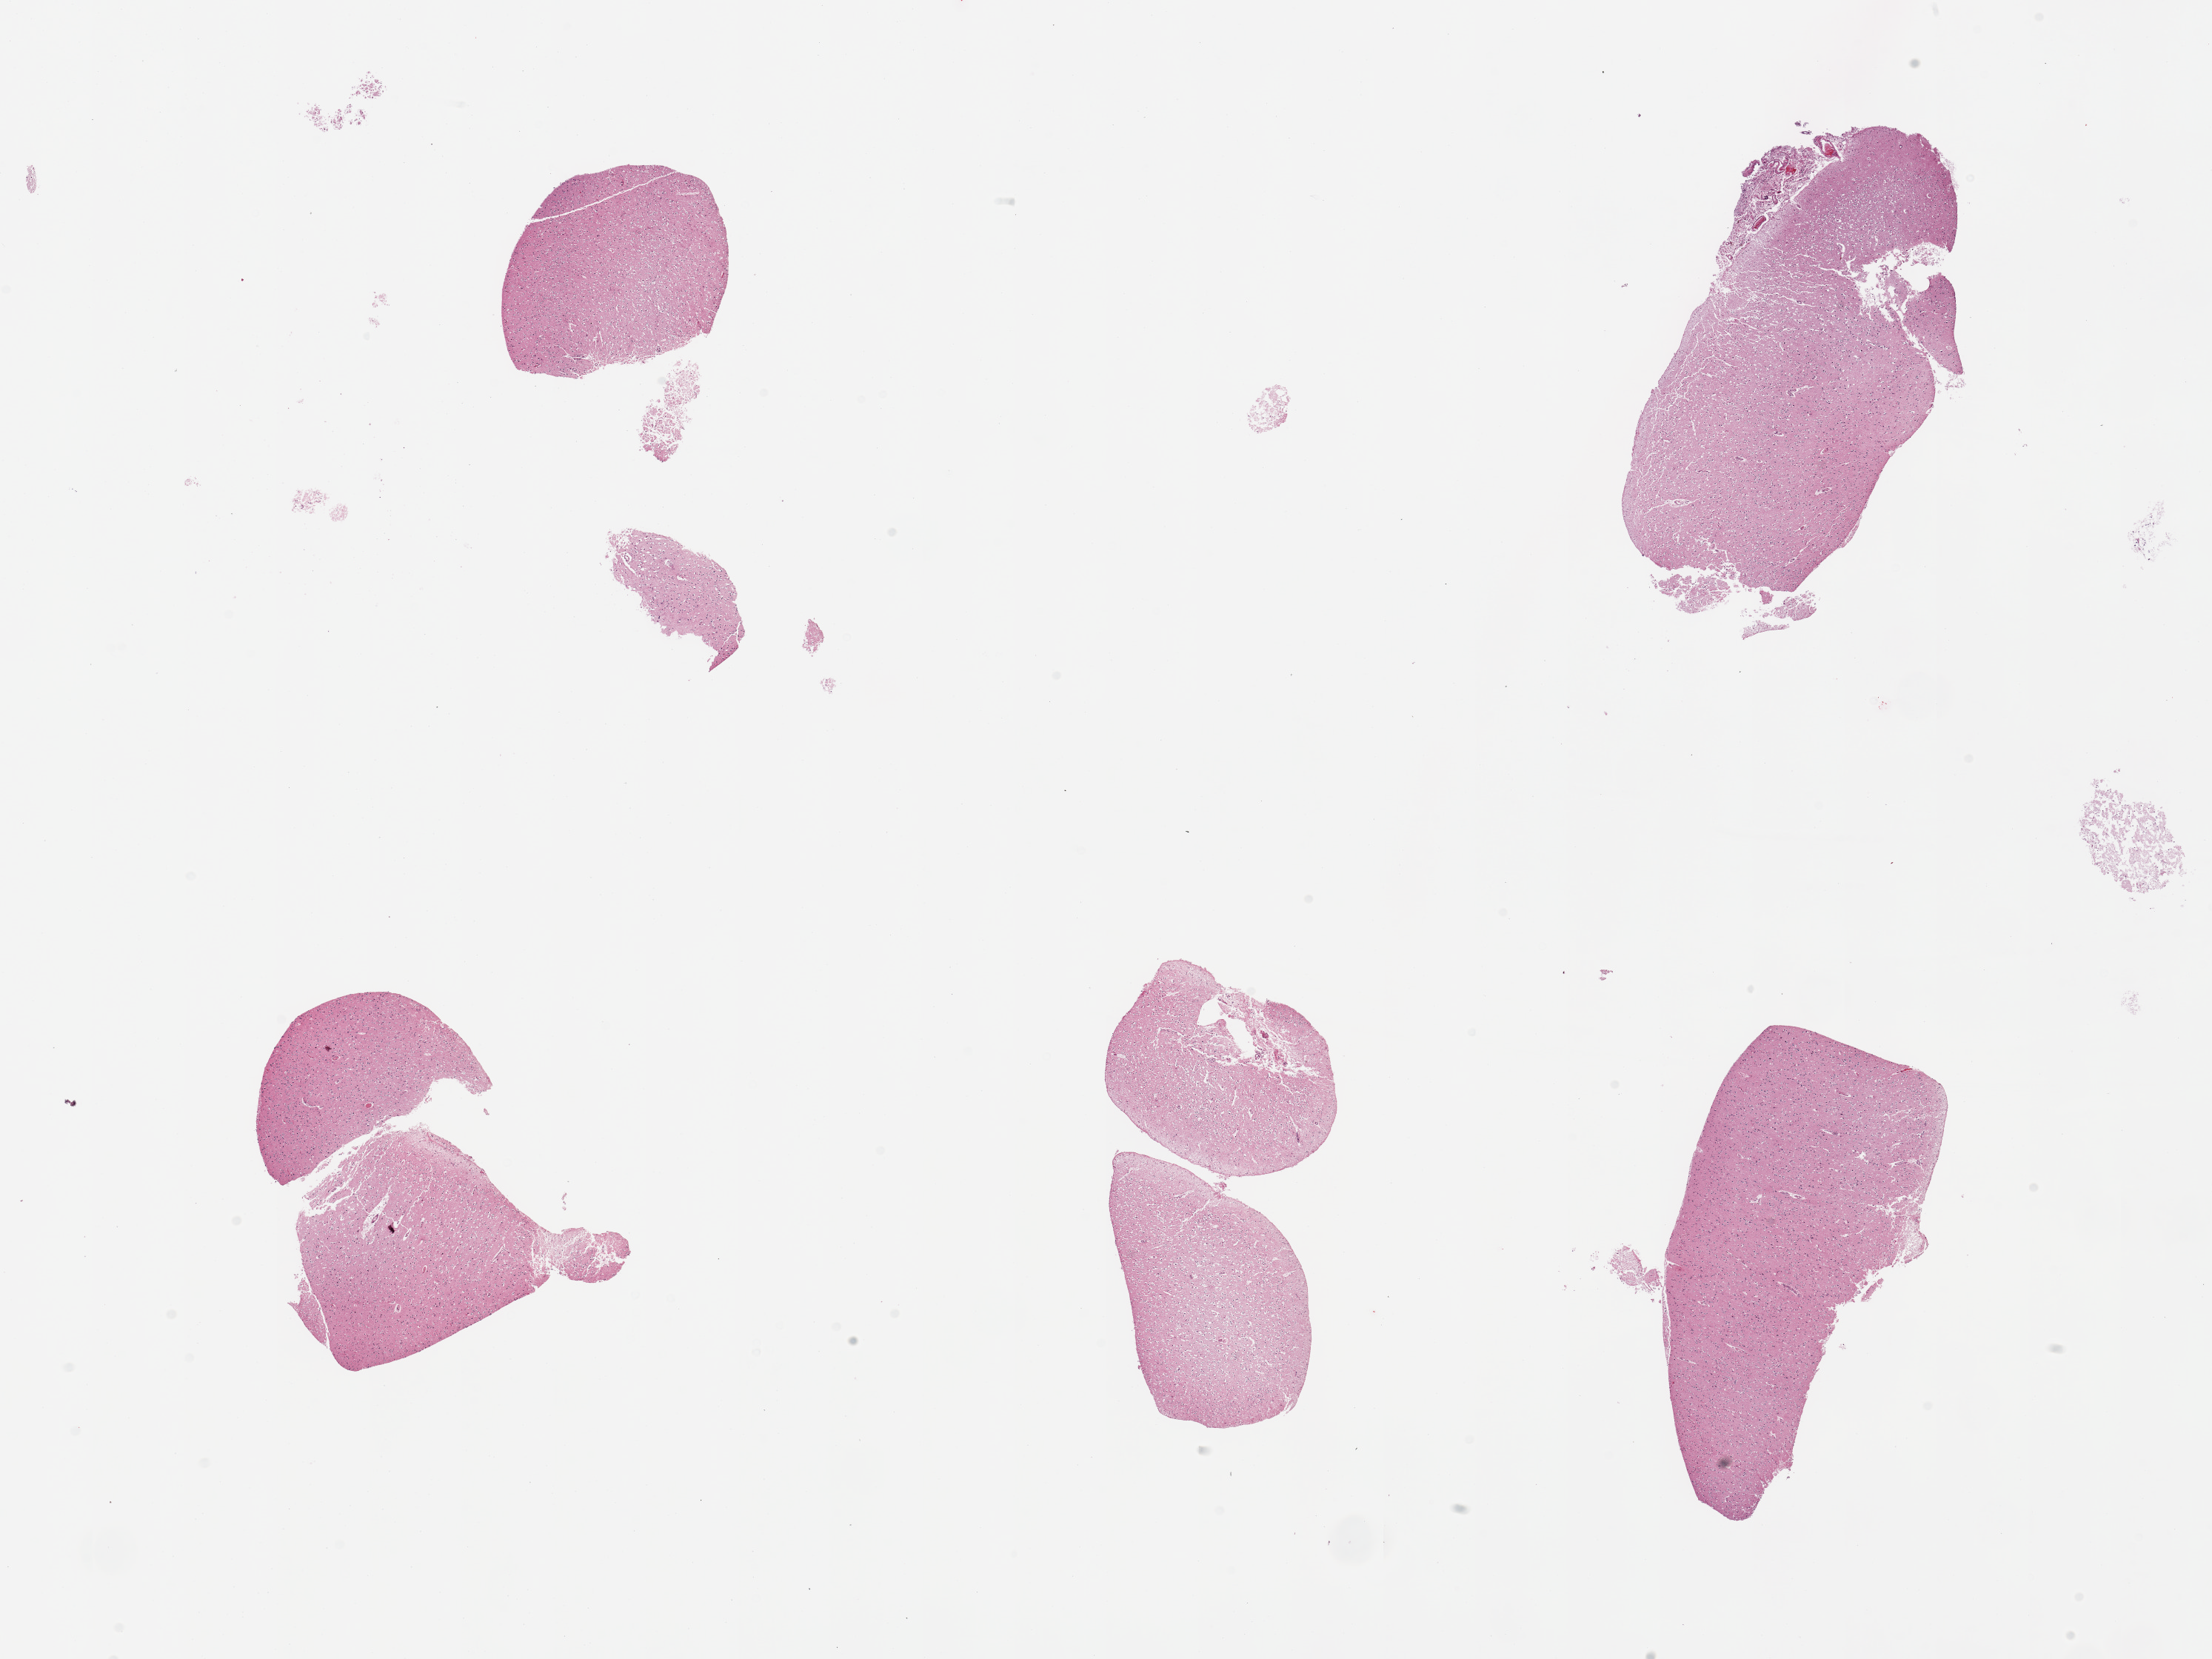
Digitized hematoxylin and eosin (H&E)-stained section, low-resolution overview of the scanned area, about 23.6 x 17.7 mm; PAXgene-fixed paraffin-embedded (PFPE) section; sampled site (target tissue): cerebral cortex; donor tissue sample.
• review note (as recorded): 5 pieces (fragmented); some increase in perinuclear halos (?hypoxic change vs autolysis)